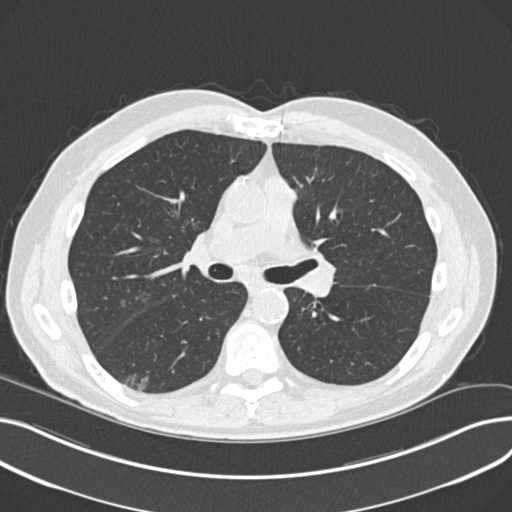
Chest CT (low-dose screening protocol), one axial image. Third screening round (two years after baseline). Lung window (W 1500 / L -600 HU). 2 mm slice thickness. Standard (soft-tissue) reconstruction kernel (B30f). Slice 104 of 230 in the series. 512 × 512 image matrix. Male participant, aged 68 years at enrolment. Current smoker at enrolment.
Expert reader's lesion annotation, bounding box (x1, y1, x2, y2) in pixels: (122, 367, 164, 398). The screening reader recorded 5 non-calcified nodules or masses ≥4 mm on this exam (right upper lobe, left upper lobe, right upper lobe, right lower lobe, right upper lobe); which of them this box marks is not recorded.